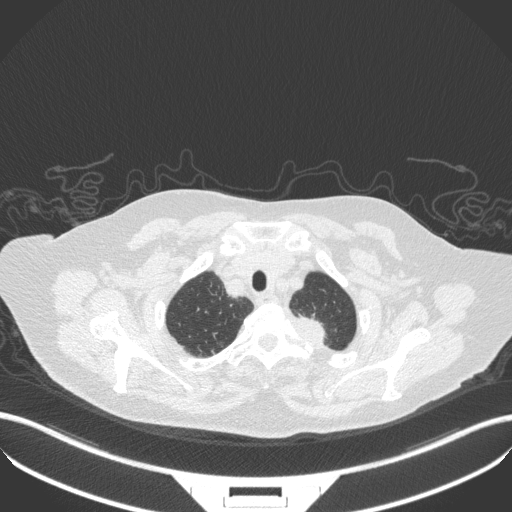
Chest CT, one axial slice; position 306 of 353 along the scan axis; reconstruction kernel B31f; 100 kVp; lung window (W 1500 / L -600 HU); 512 × 512 image matrix. Female patient, age 81 years. From the clinical record (not read from this slice): clinical TNM (as recorded): T2a N0 M0.
Outlined on this slice (rectangle marked by the reading radiologist):
- lung tumour (recorded histology: adenocarcinoma): bounding box [x1, y1, x2, y2] px = [290, 314, 340, 357]